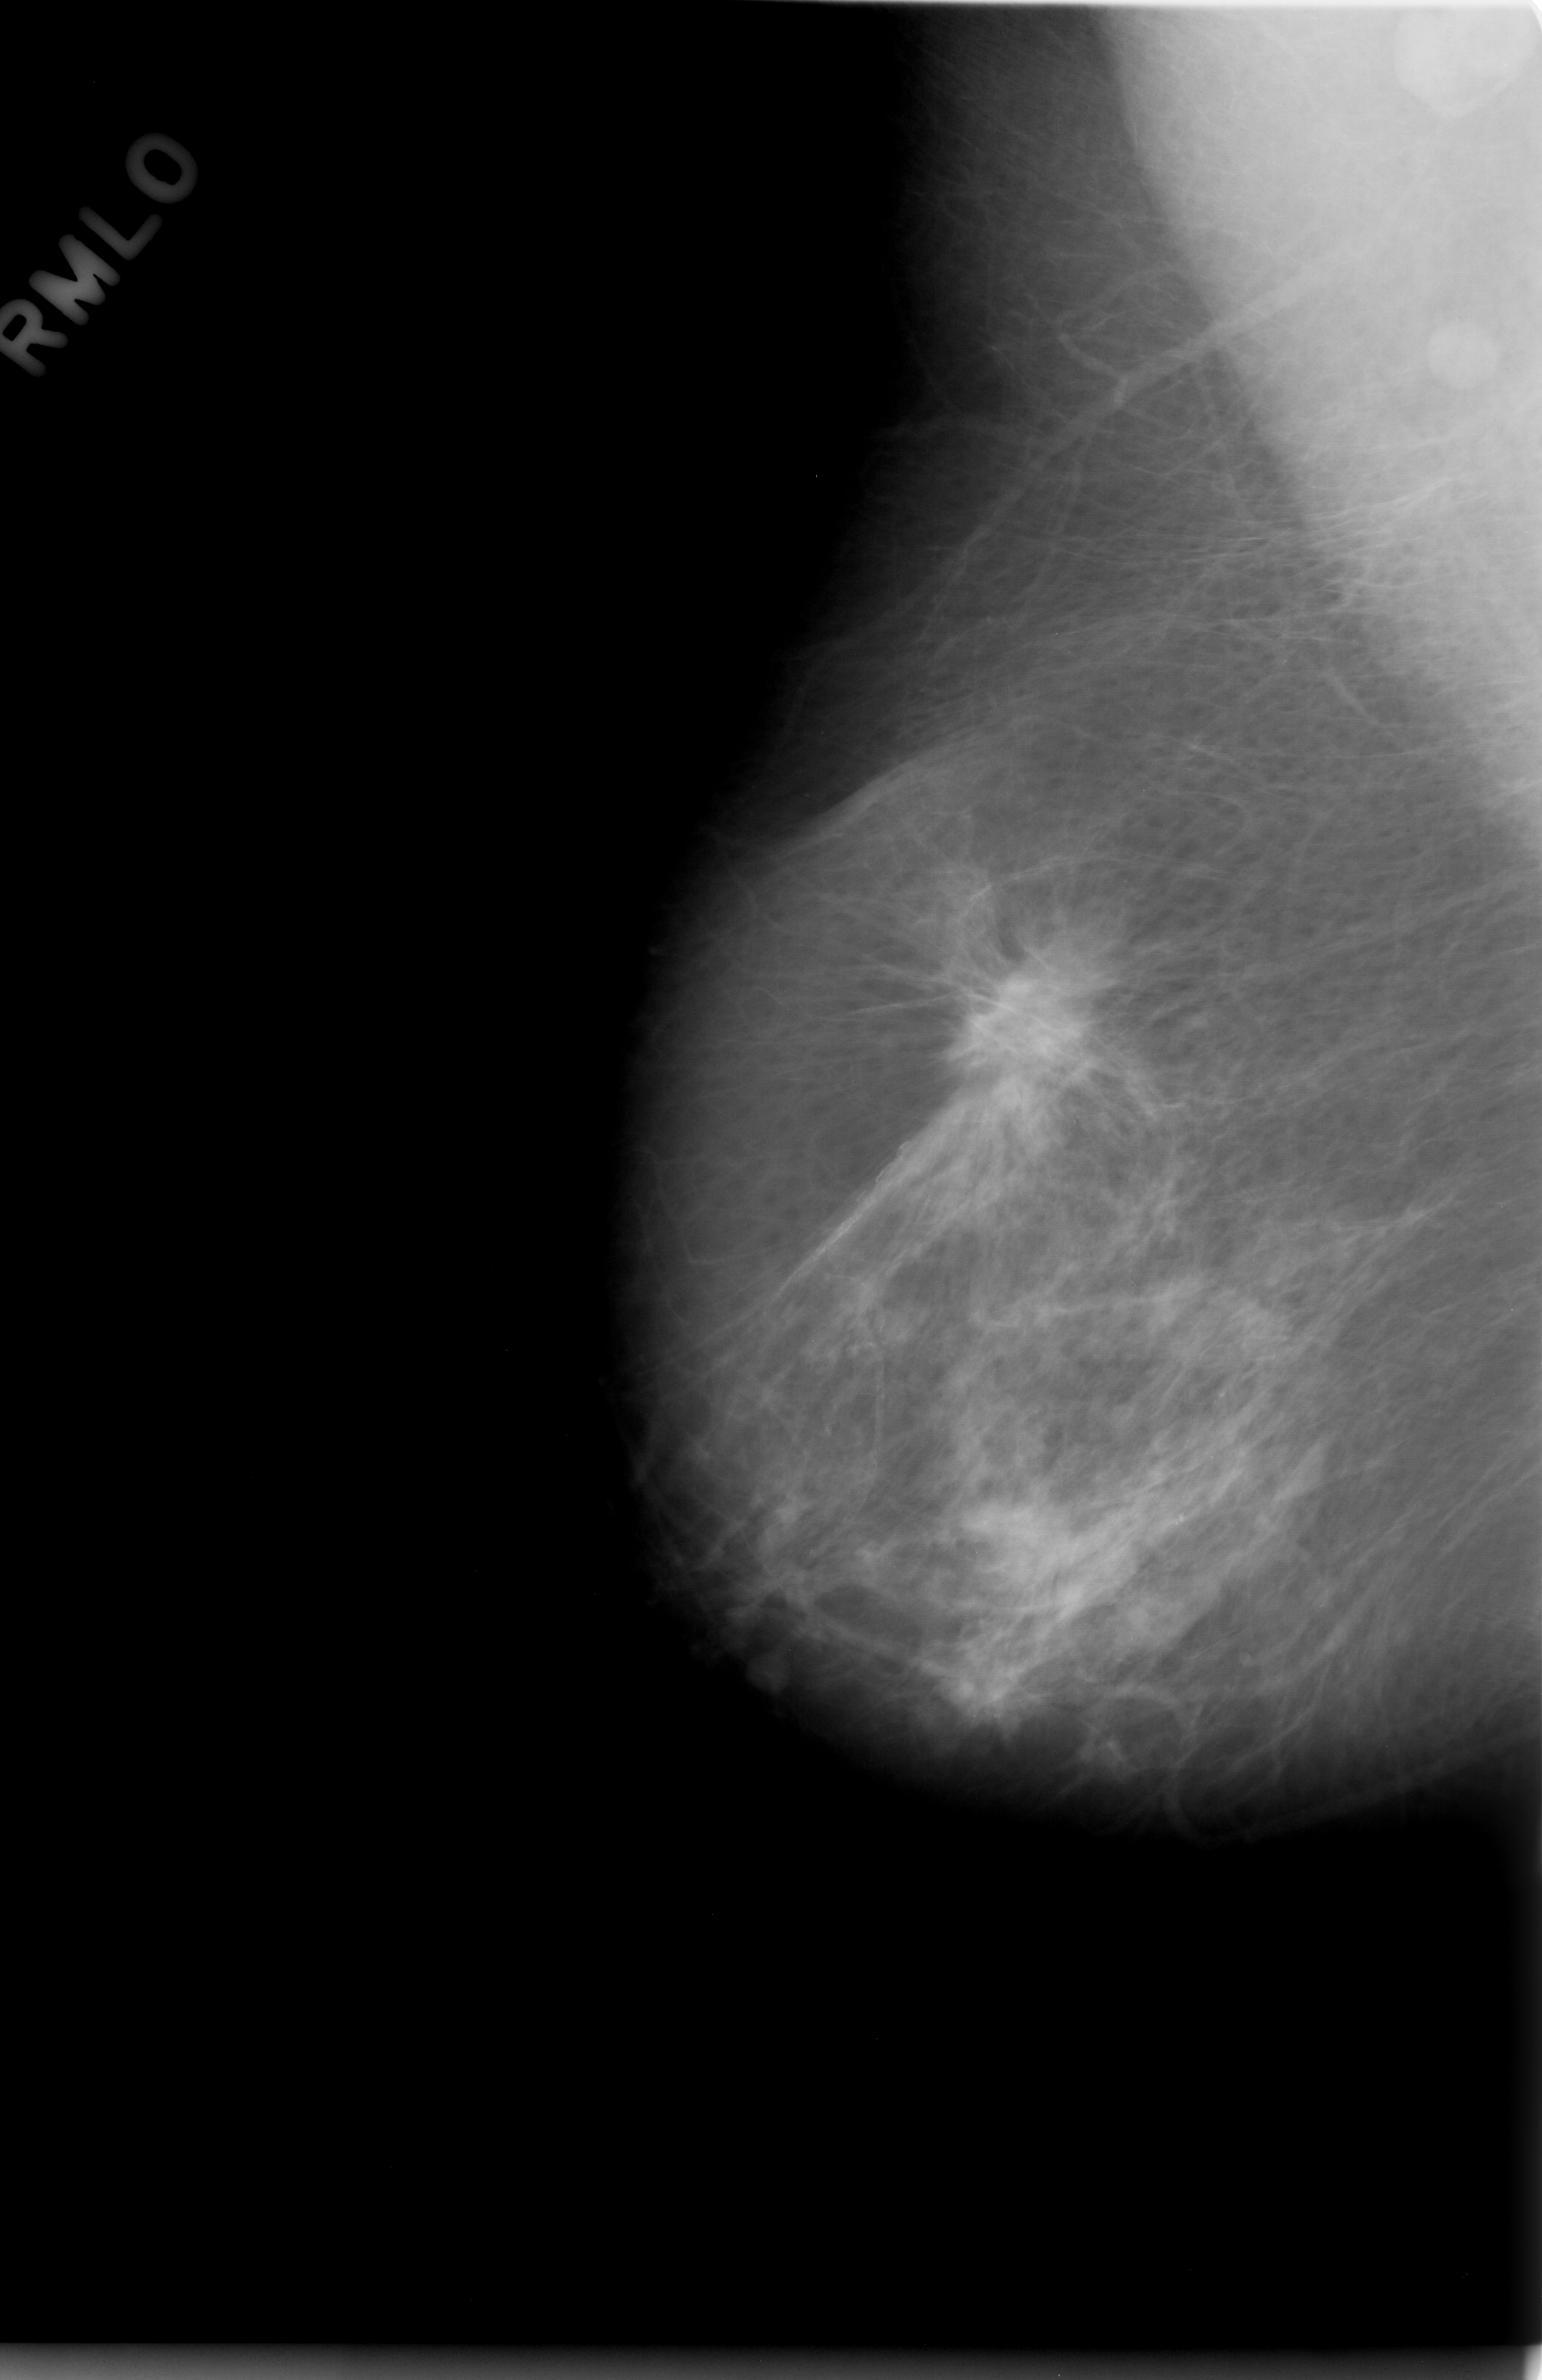
Scanned film-screen mammogram, right breast, mediolateral oblique (MLO) view.
Finding: mass, shape architectural distortion, margins spiculated; BI-RADS assessment category 2; pathology result (as recorded, not read from the image): benign.